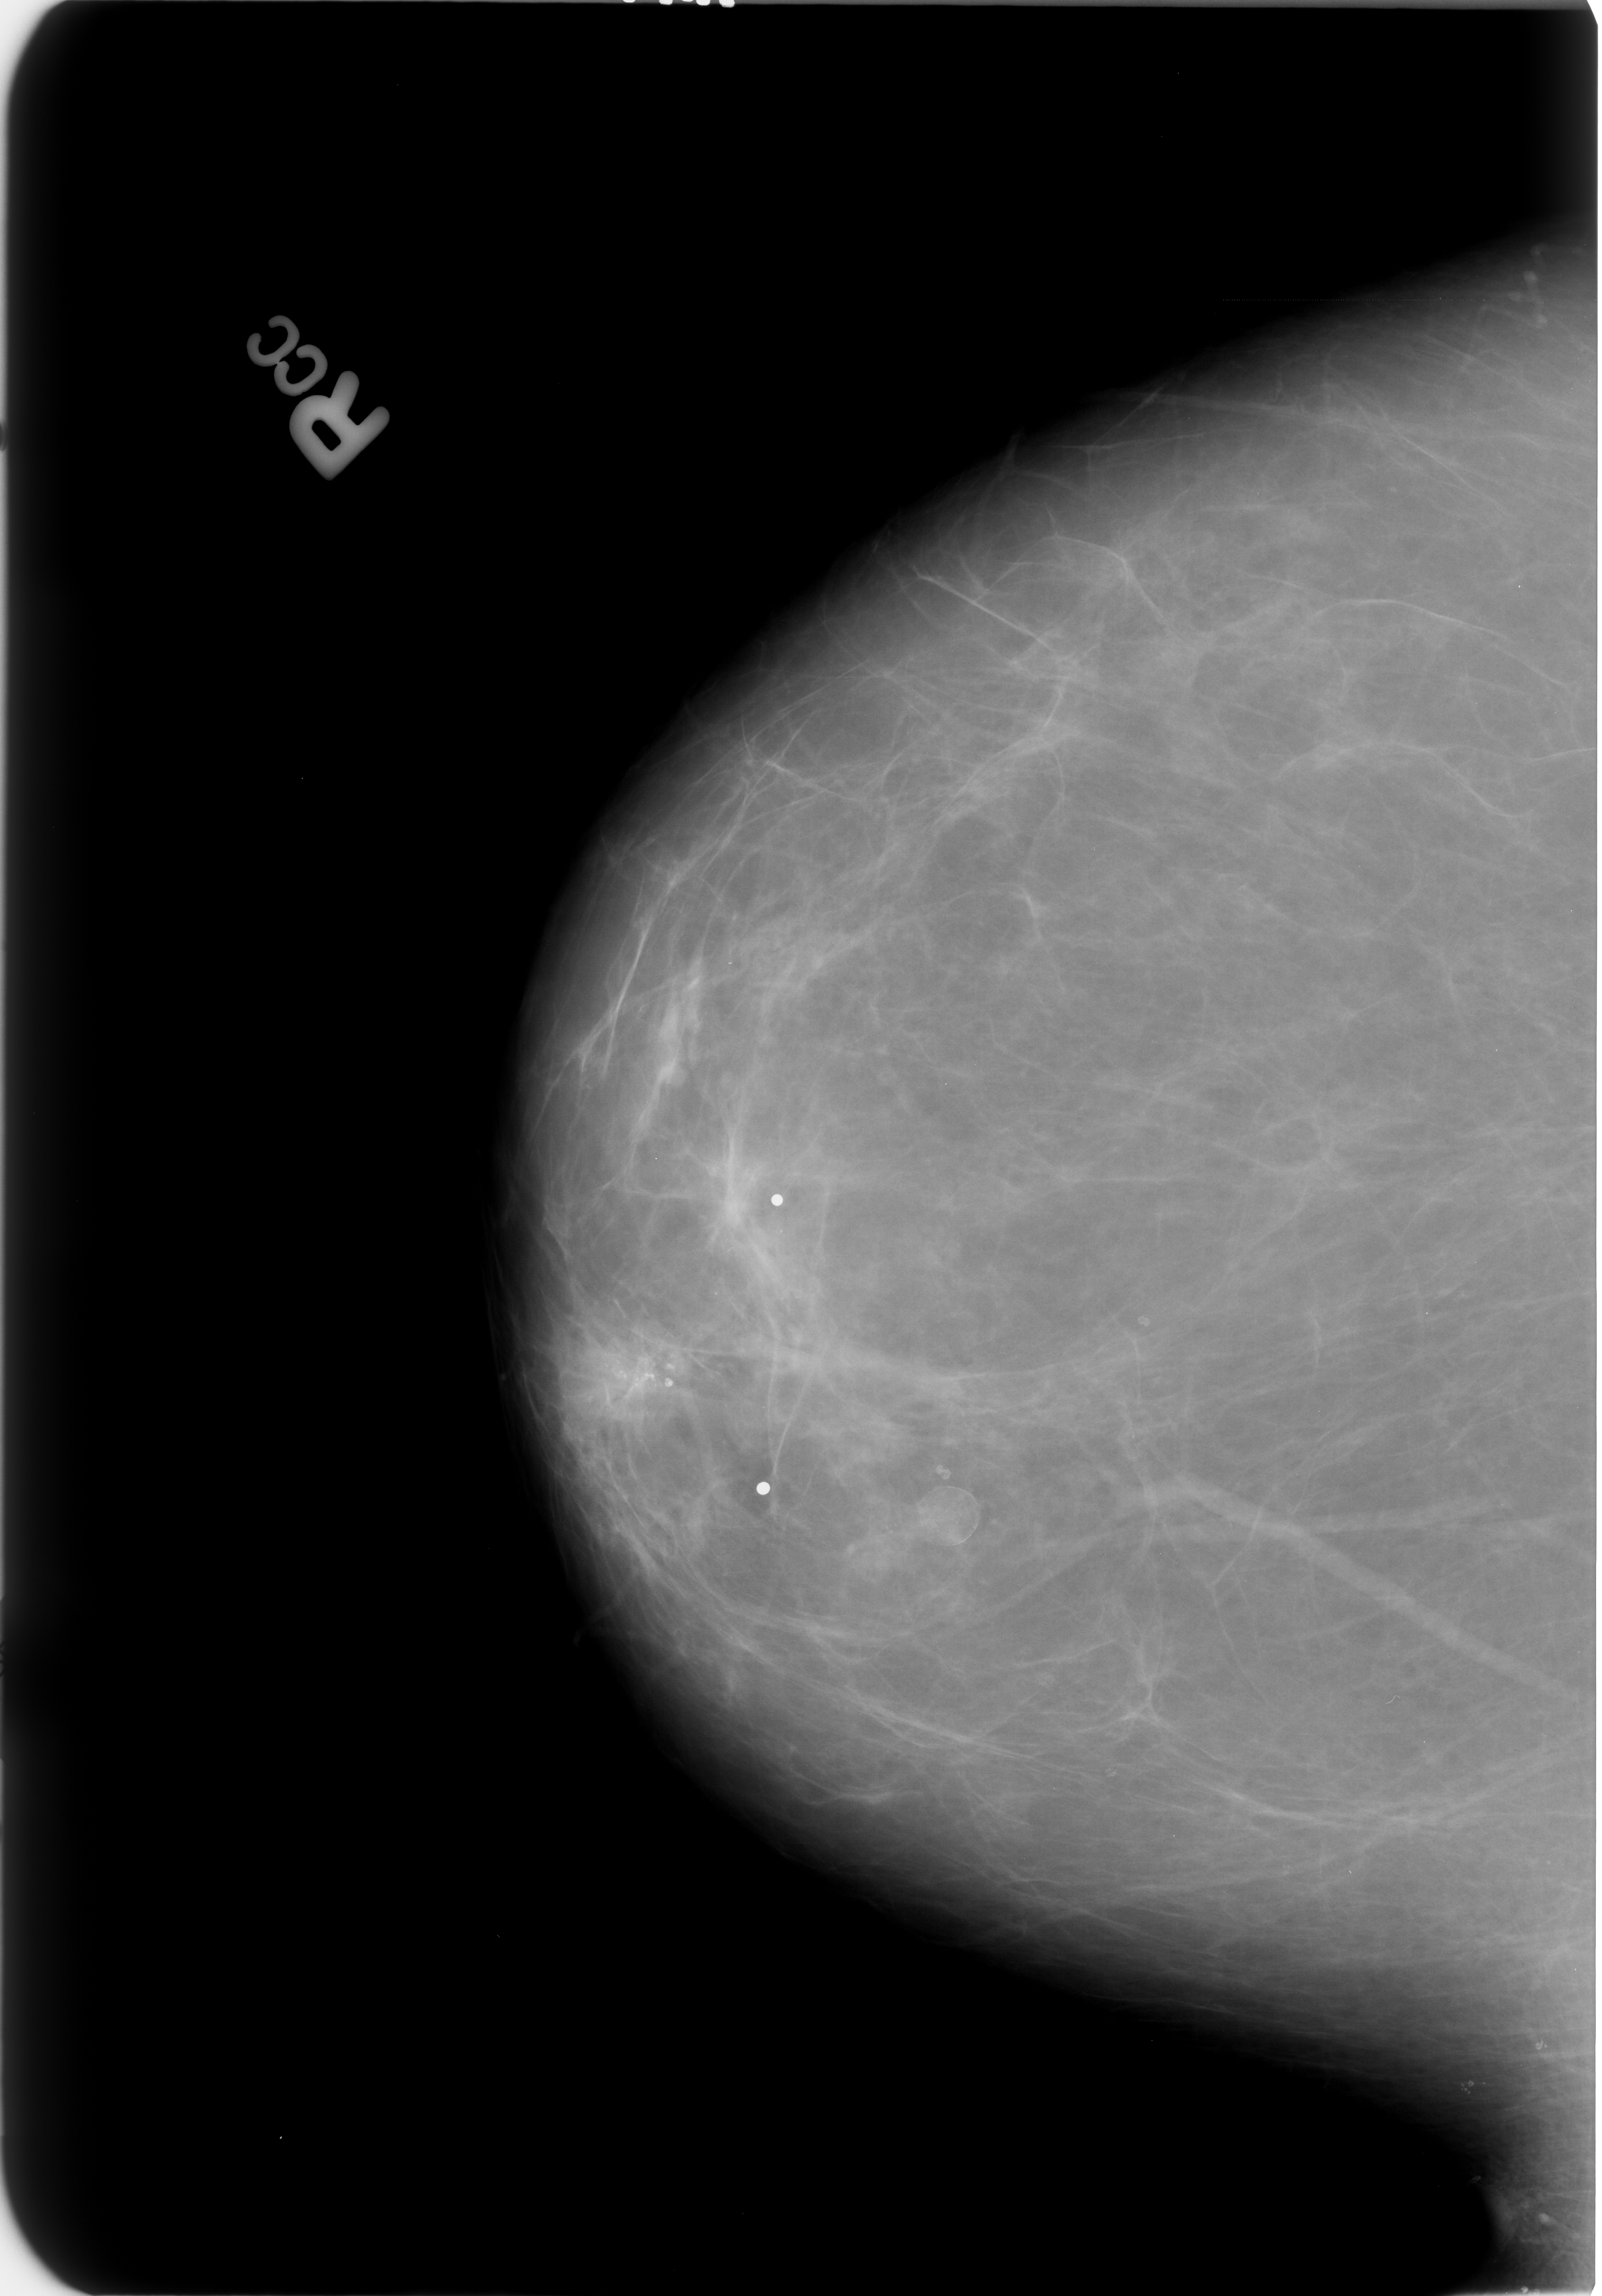
Mammogram (digitized film); right breast; CC view; BI-RADS breast density category 1 (scale 1–4).
- Abnormality record for this image: calcifications, morphology pleomorphic, distribution clustered; BI-RADS assessment category 4; pathology (as recorded): benign.